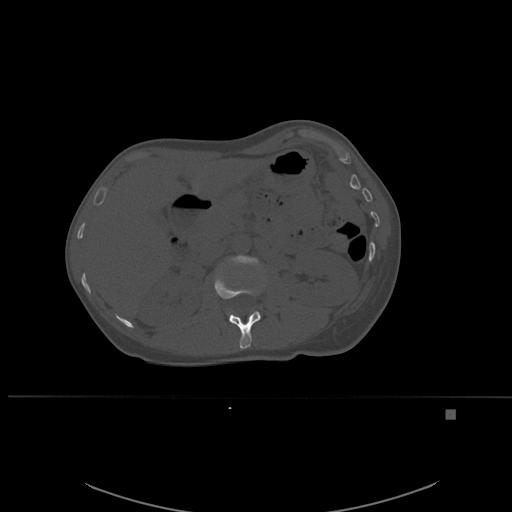
CT including the spine, one axial slice. Slice 251 of 537 in the series (ordered by position). Bone window (W 1800 / L 400 HU). 512 × 512 image matrix. Patient: female, 45 years. From the clinical record (not read from this slice): primary cancer: lung.
Annotated regions visible in this slice (semi-automatic segmentation, software-assisted and operator-edited):
- L1 vertebra: bounding box <214,269,261,349> (left, top, right, bottom; pixels)
- L2 vertebra: <230,255,259,269>